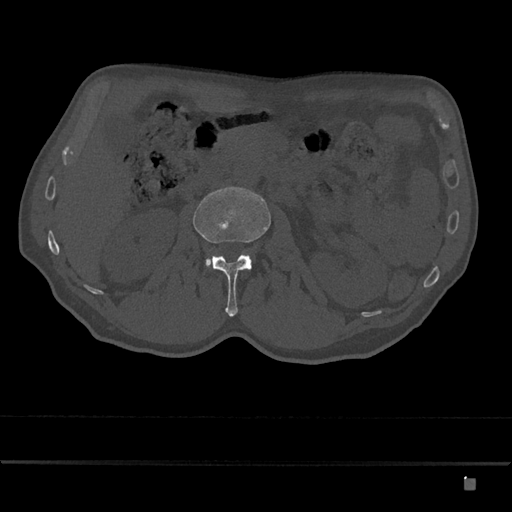
CT including the spine, one axial slice. Slice 463 of 797 in the series (ordered by position). Bone window (W 1800 / L 400 HU). 512 × 512 image matrix, field of view 390 × 390 mm. Male patient, age 72 years. Case-level facts recorded for this patient, not image findings: primary cancer: prostate.
Structures marked on this image (semi-automatically segmented with operator editing):
- L2 vertebra: bounding box (x1, y1, x2, y2) in pixels: (193, 187, 271, 317)
- L3 vertebra: (205, 257, 213, 267)